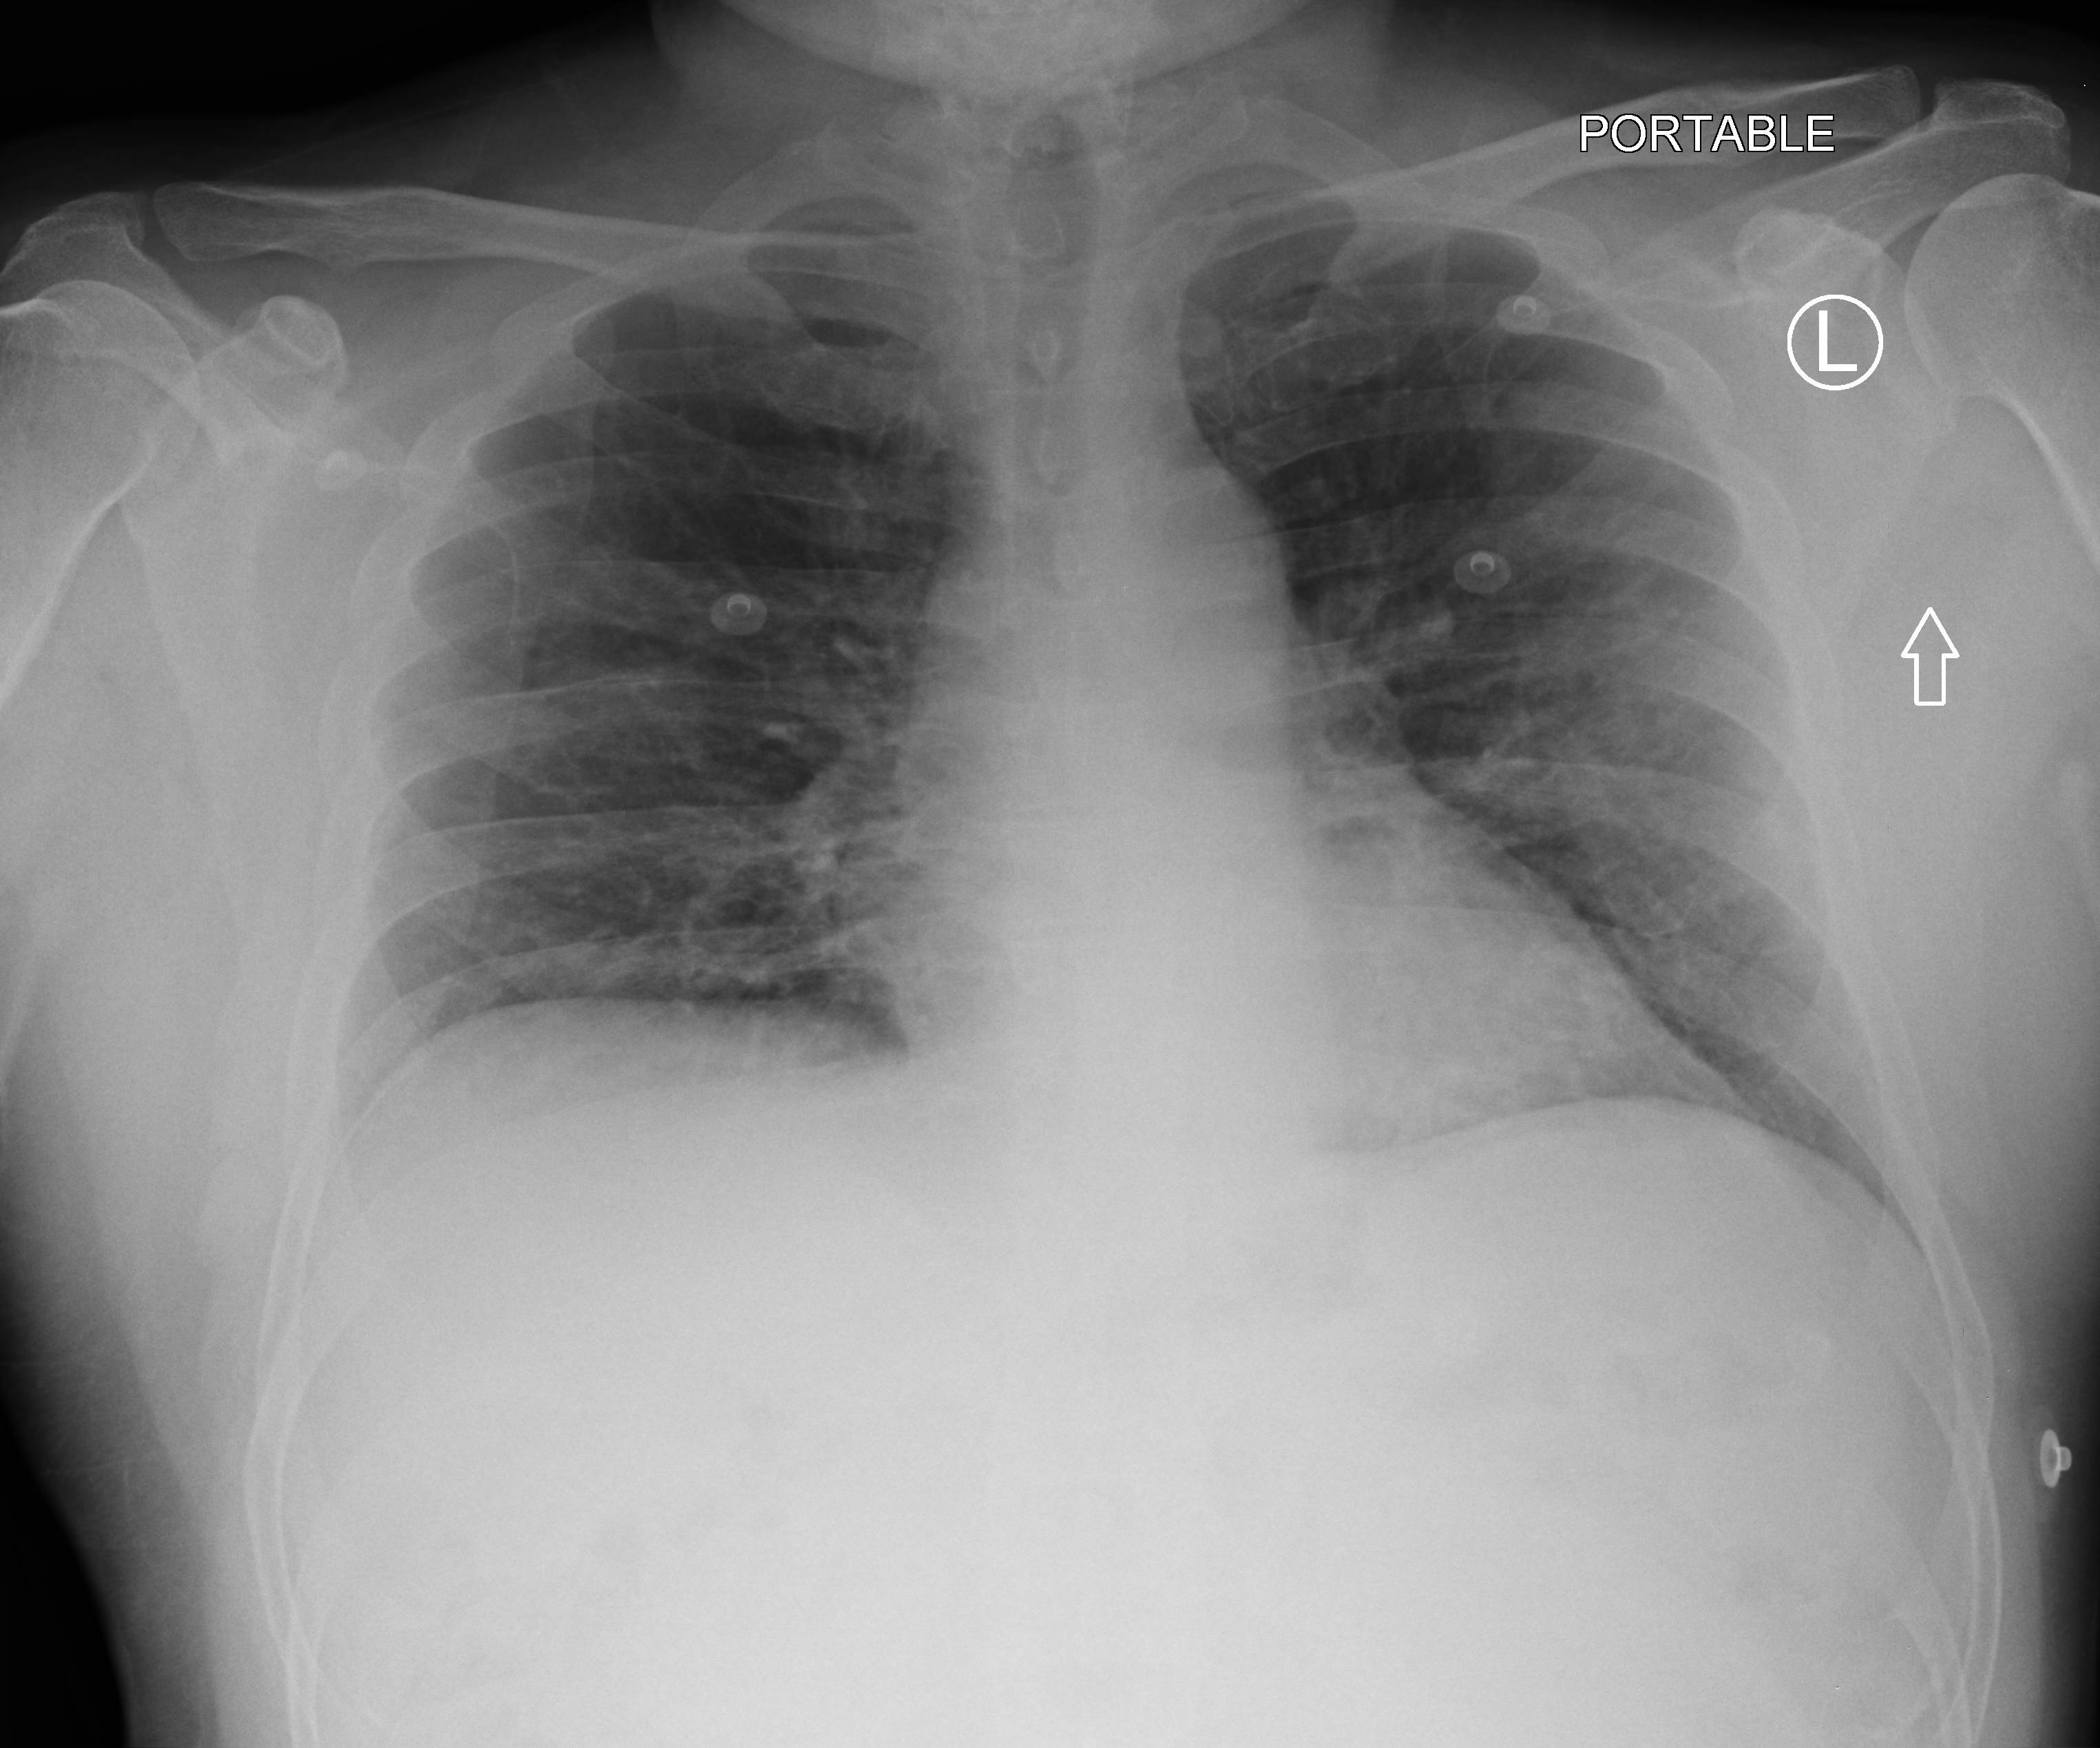
Portable chest radiograph; anteroposterior (AP) projection. Patient hospitalised with COVID-19; male, aged 18–59 years.
Hospital-stay facts (about this admission, not read from this image; timing relative to this image not recorded): diabetes (admission record): no; admitted to intensive care during this hospital stay: no; smoking status (admission record): never.